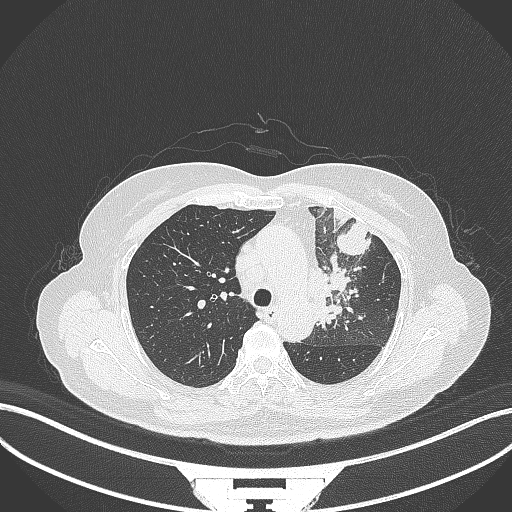
Chest CT, one axial slice. Reconstruction kernel B70f. 120 kVp. Lung window (W 1500 / L -600 HU). 1 mm slice thickness. 512 × 512 image matrix, field of view 400 × 400 mm. Patient: female, 64 years. Case-level facts recorded for this patient, not image findings: clinical TNM (as recorded): T2a N2 M0.
Structures marked on this image (rectangle marked by the reading radiologist):
- lung tumour (recorded histology: adenocarcinoma): bounding box (x1, y1, x2, y2) in pixels: (308, 253, 362, 328)
- lung tumour (recorded histology: adenocarcinoma): (333, 221, 371, 260)